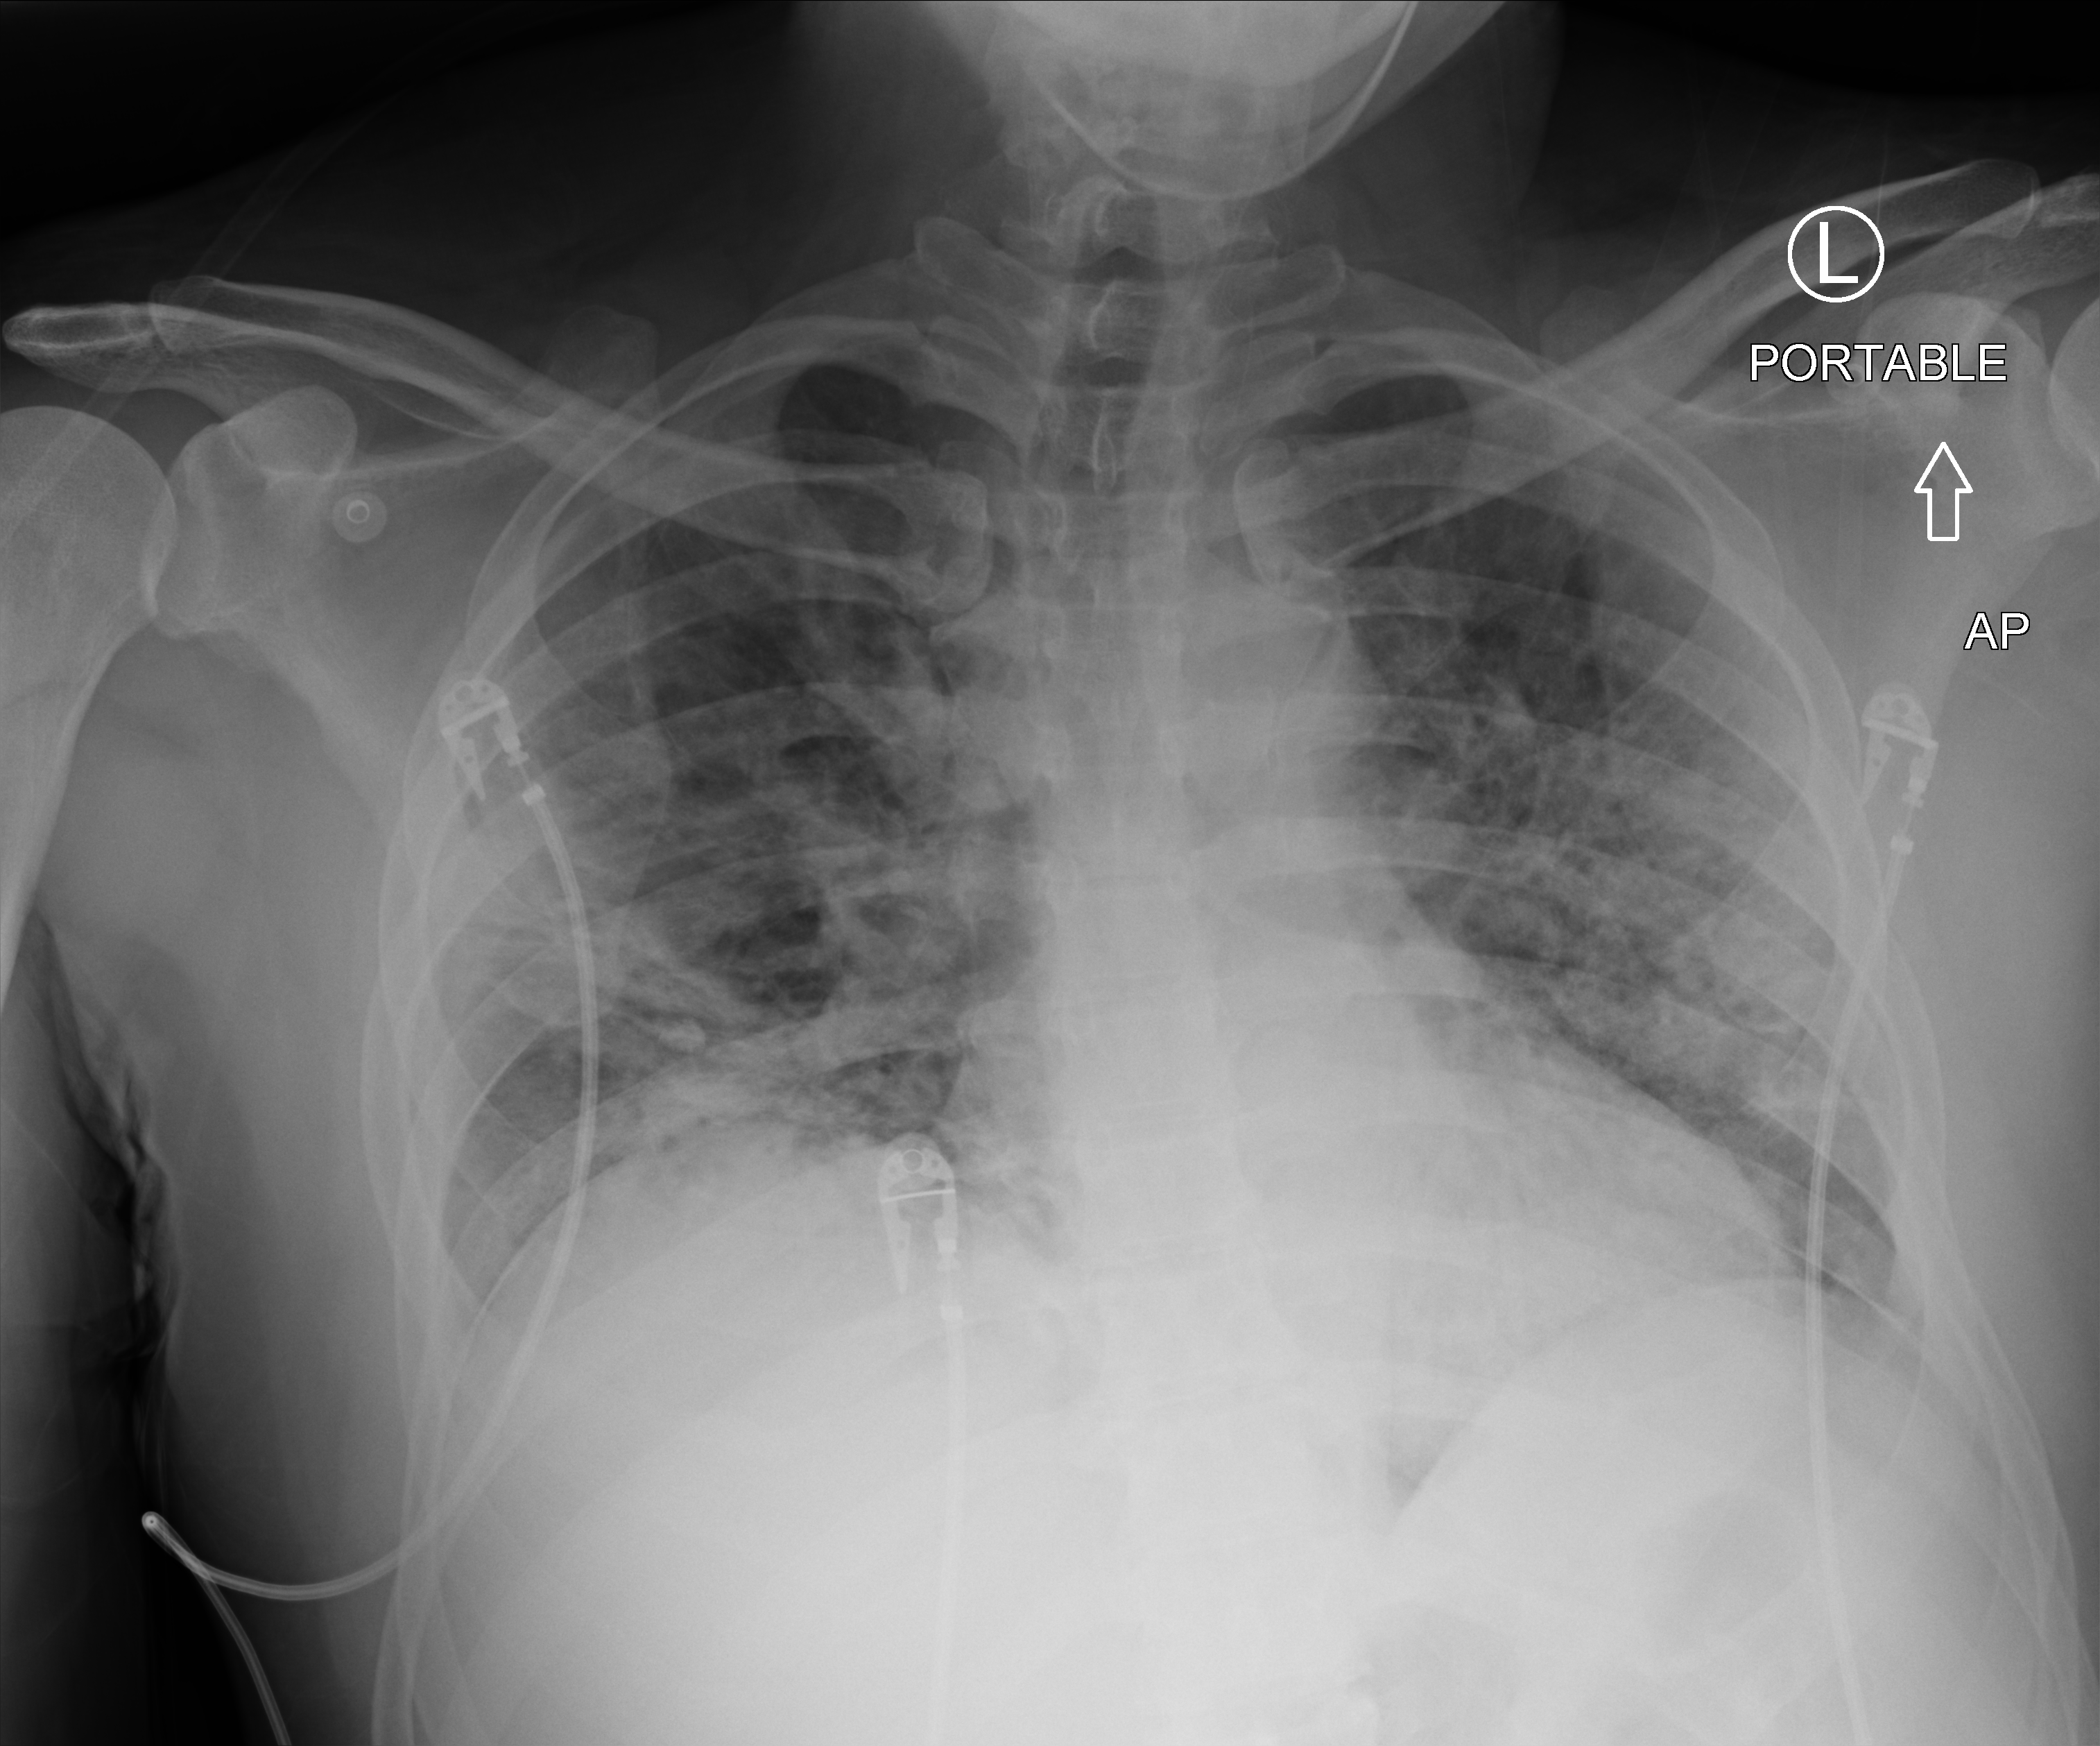
Bedside chest radiograph (computed radiography). Patient hospitalised with COVID-19; male, aged 18–59 years.
Hospital-stay facts (about this admission, not read from this image; timing relative to this image not recorded): length of hospital stay: 15 days; mechanically ventilated during this hospital stay: yes.